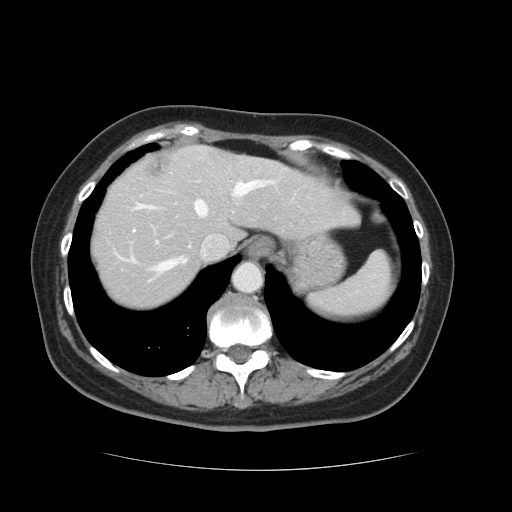
Contrast-enhanced abdominal CT, one axial slice; slice 104 of 128 in the series (ordered by position); 120 kVp; intravenous contrast given; soft-tissue window (W 400 / L 40 HU); 512 × 512 image matrix. Female patient, age 67 years. Case-level facts recorded for this patient, not image findings: diagnosis: colorectal cancer liver metastases, imaged before liver resection; multiple liver metastases: yes; largest metastasis: 3 cm.
Outlined on this slice (manually delineated by an expert):
- hepatic veins: bounding box (x1, y1, x2, y2) in pixels: (126, 181, 266, 282)
- liver: (90, 146, 354, 308)
- planned liver remnant (the part of the liver to remain after resection): (90, 157, 354, 309)
- portal vein (with intrahepatic branches): (197, 180, 199, 182)
- liver metastasis: (145, 160, 164, 179)